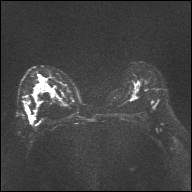
Breast MRI, one axial slice; position 19 of 32 along the scan axis; diffusion-weighted series; image 2 of 4 stored at this slice position (different b-values; order by instance number); 1.5 T; 192 × 192 image matrix, field of view 360 × 360 mm. Female patient.
Annotated regions visible in this slice (expert manual segmentation):
- tumour on diffusion-weighted imaging: bounding box [x1, y1, x2, y2] px = [35, 87, 42, 93]